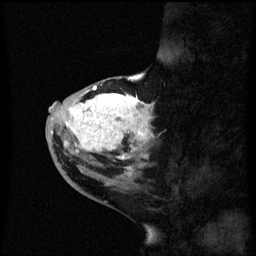
Breast MRI (dynamic contrast-enhanced), one sagittal slice; slice 24 of 60 in the series (ordered by position); dynamic contrast-enhanced series, image 2 of 3 at this slice position (ordered by acquisition); 1.5 T; TE 4.2 ms, TR 8.4 ms; 2.3 mm slice thickness; 256 × 256 image matrix, field of view 200 × 200 mm. Female patient, age 46 years. From the clinical record (not read from this slice): setting: breast cancer imaged before/during neoadjuvant chemotherapy; receptor status: HER2-positive.
Annotated regions visible in this slice (semi-automatic segmentation, software-assisted and operator-edited):
- analysis volume of interest (the breast-tissue region the enhancement analysis was run in; not a lesion): bounding box [x1, y1, x2, y2] px = [46, 86, 155, 171]
- tumour enhancement mask (voxels above the 70 % enhancement threshold inside the analysis volume of interest): [54, 86, 153, 171]